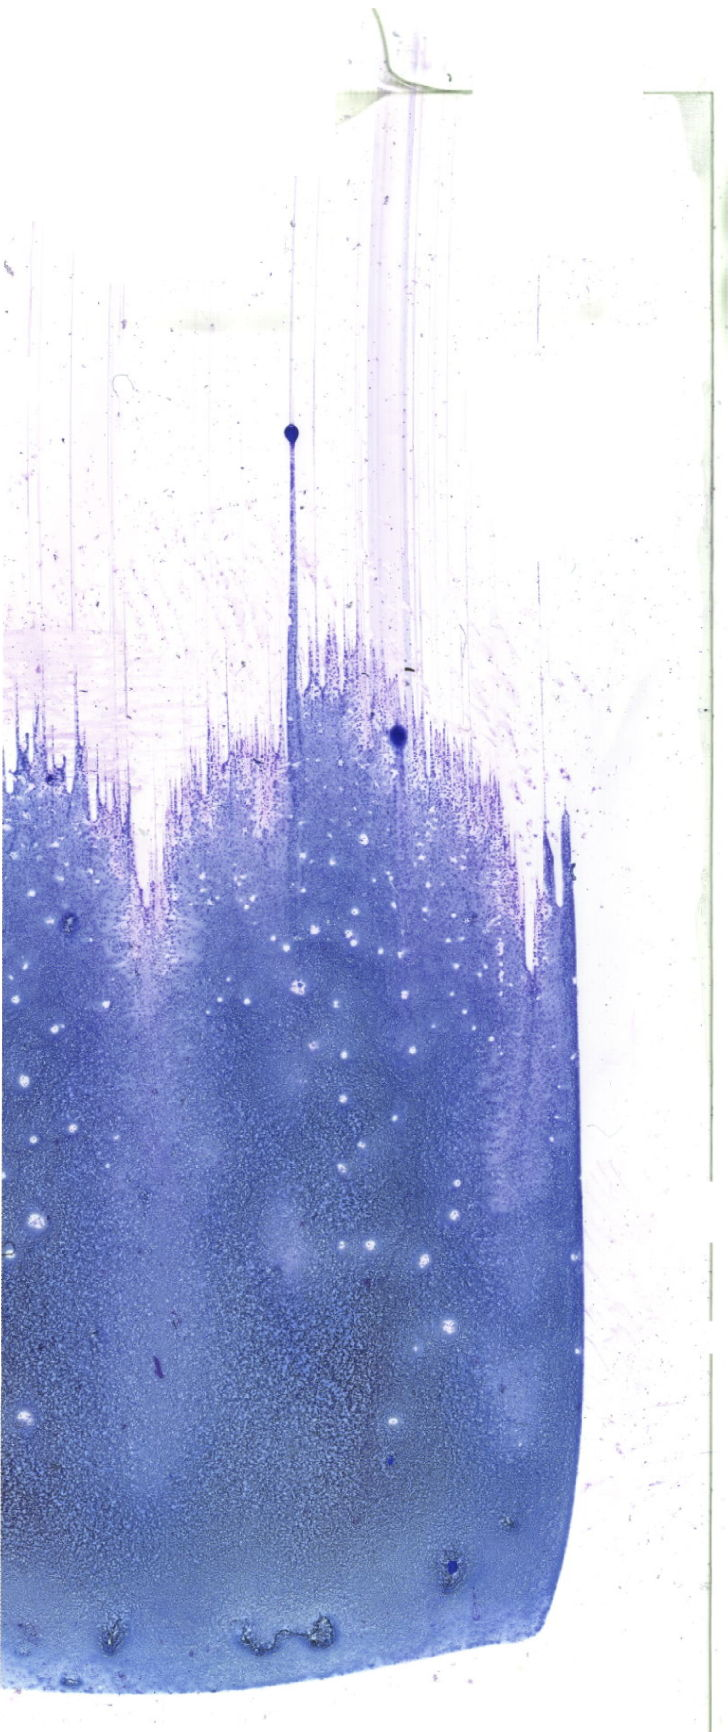
Bone marrow aspirate smear, May-Grünwald–Giemsa stain, whole-slide image — low-resolution overview of the scanned area, about 20.6 x 49.1 mm. Female patient.
Diagnosis: Acute Monocytic Leukemia.